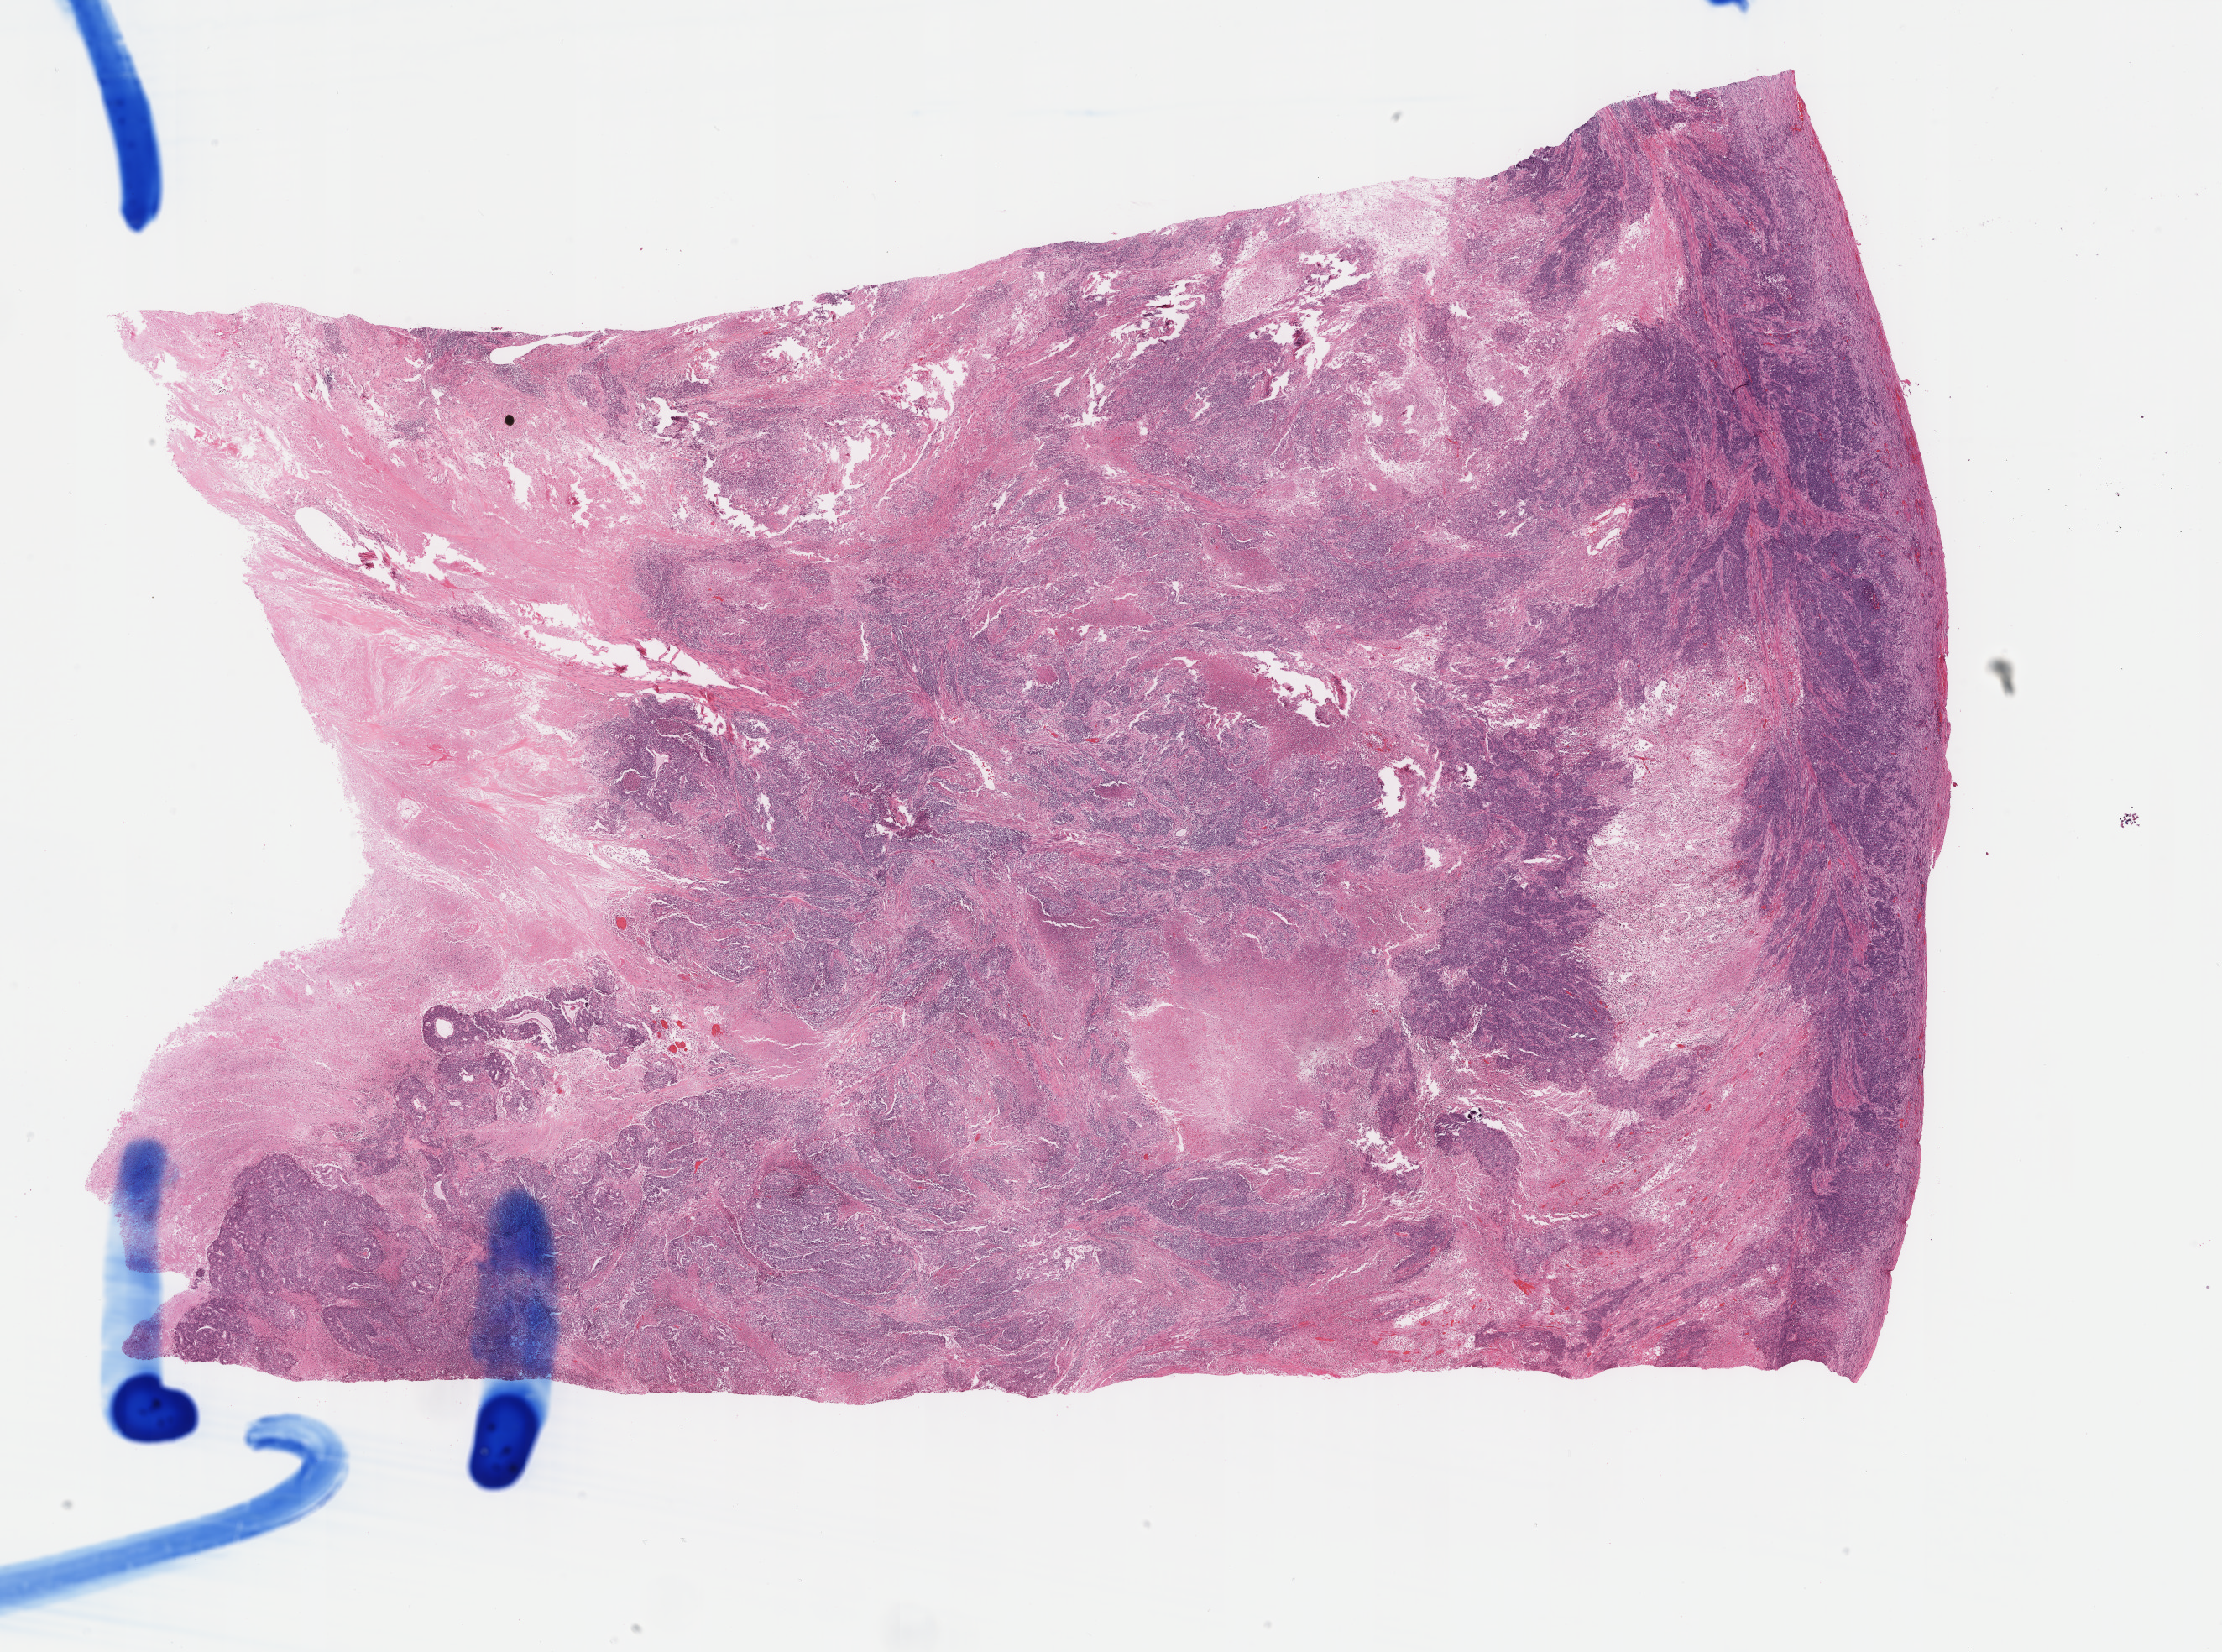
Whole-slide histology image, Hematoxylin and eosin (H&E) stained, whole scanned area (about 21.0 x 15.6 mm, slide scanned at 40x) shown as a low-resolution overview; FFPE section; primary tumour sample from the uterus. Female, age 47 years at initial diagnosis. Histologic grade: G3 (poorly differentiated).
• lymph nodes positive (case pathology): 1 of 2 examined
• pathologic diagnosis: Endometrioid adenocarcinoma, NOS (endometrium)
• FIGO stage: IIIC